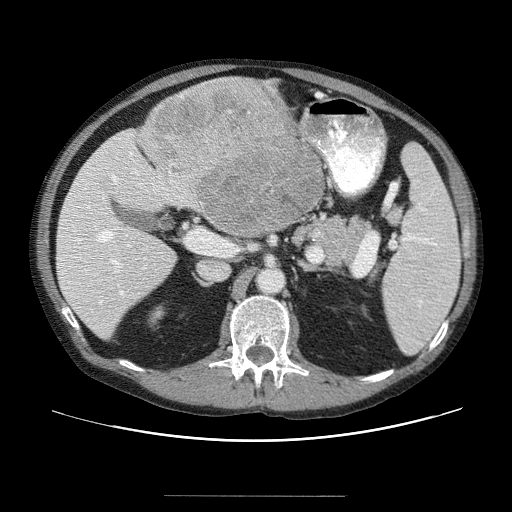
Contrast-enhanced abdominal CT (liver protocol), one axial slice; slice 20 of 69 in the series (ordered by position); 120 kVp; soft-tissue window (W 400 / L 40 HU); 2.5 mm slice thickness; 512 × 512 image matrix. From the clinical record (not read from this slice): diagnosis: hepatocellular carcinoma (patient treated with transarterial chemoembolisation; whether this scan precedes or follows treatment is not stated here); TNM stage (as recorded): Stage-IVB; Child-Pugh class: B; tumour differentiation: poorly differentiated; tumour nodularity: multinodular.
Annotated regions visible in this slice (semi-automatic segmentation, software-assisted and operator-edited):
- liver parenchyma outside the tumour (the mass and vessels are separate outlines, so this box may not span the whole liver): box from (x=56, y=108) to (x=330, y=334) px
- mass: (x=141, y=79)–(x=329, y=239)
- liver vessels: (x=62, y=157)–(x=155, y=318)